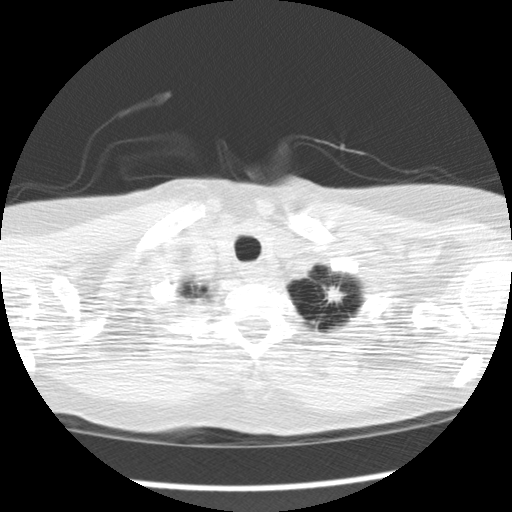
Low-dose screening chest CT, one axial slice; slice 151 of 159 in the series (ordered by position); reconstruction kernel STANDARD; 120 kVp; lung window (W 1500 / L -600 HU); 512 × 512 image matrix.
Structures marked on this image (expert manual segmentation):
- lesion 1 (tumor, upper lobe of left lung): bounding box [x1, y1, x2, y2] px = [324, 286, 344, 303]